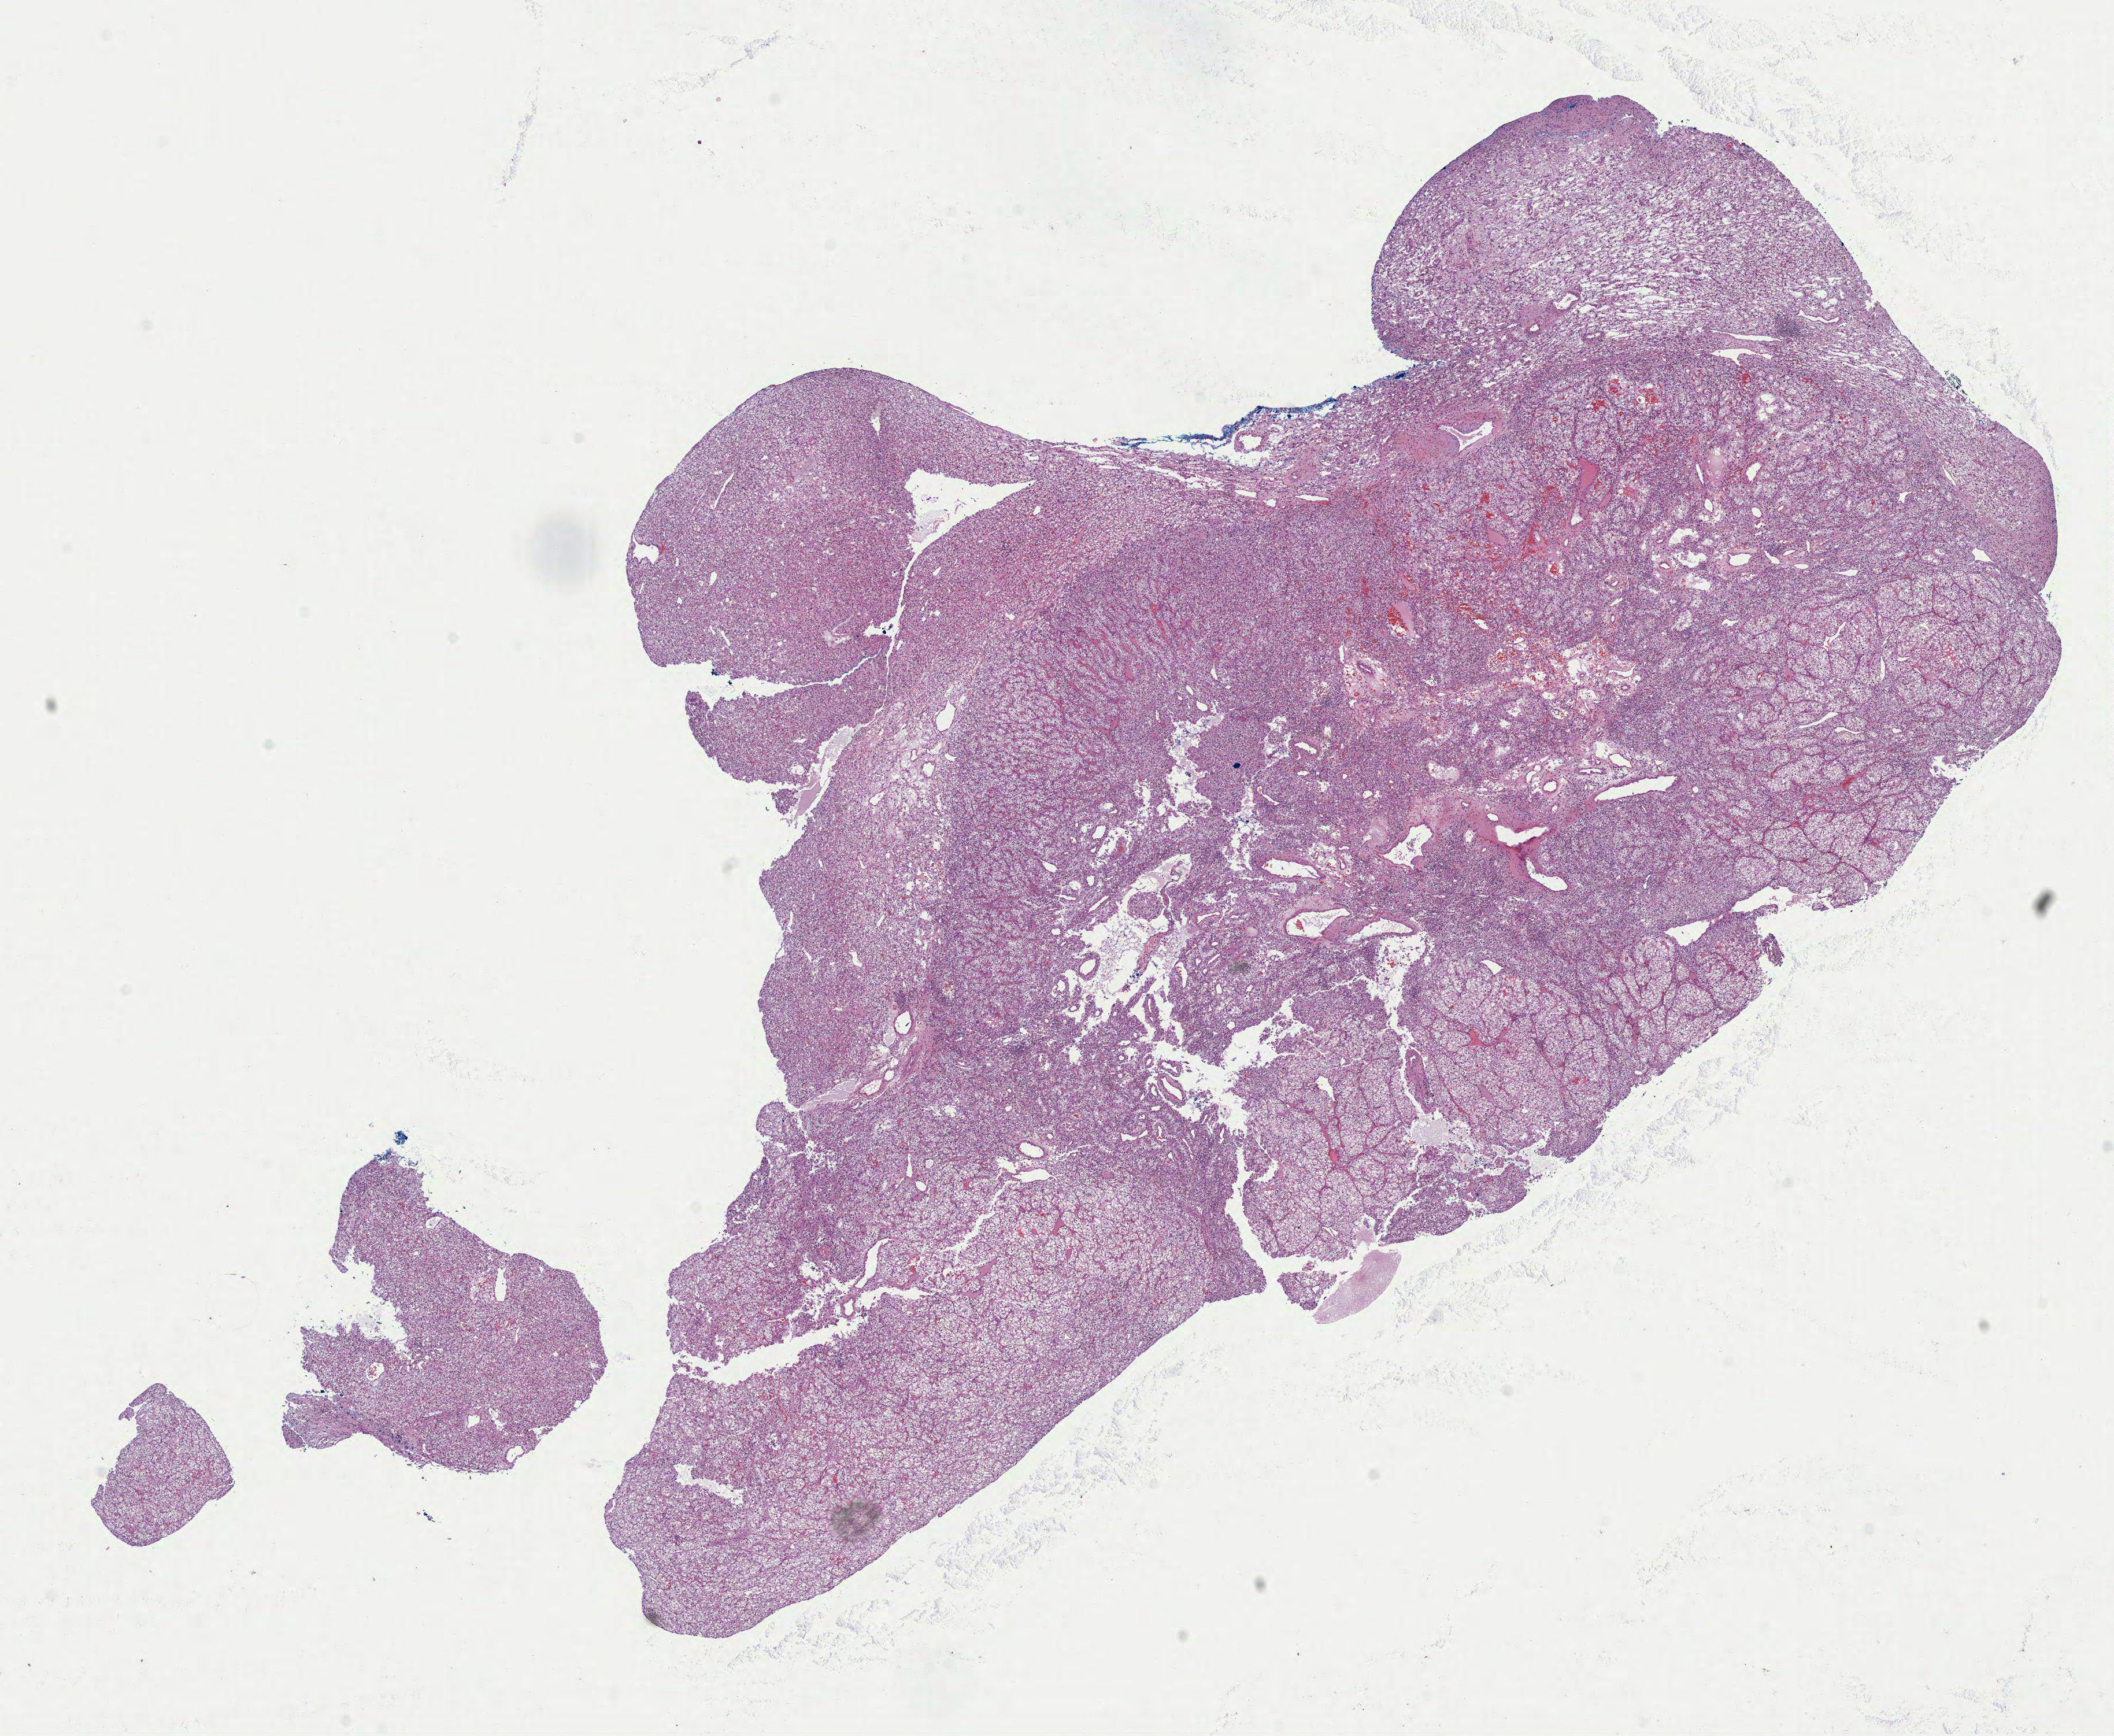
H&E-stained whole-slide image — a low-resolution overview of the entire scanned area, about 14.7 x 12.1 mm (slide scanned at 40x), formalin-fixed paraffin-embedded (FFPE) diagnostic section, kidney, primary tumour sample. Female, age 74 years at initial diagnosis.
Histologic diagnosis: Clear cell adenocarcinoma, NOS.